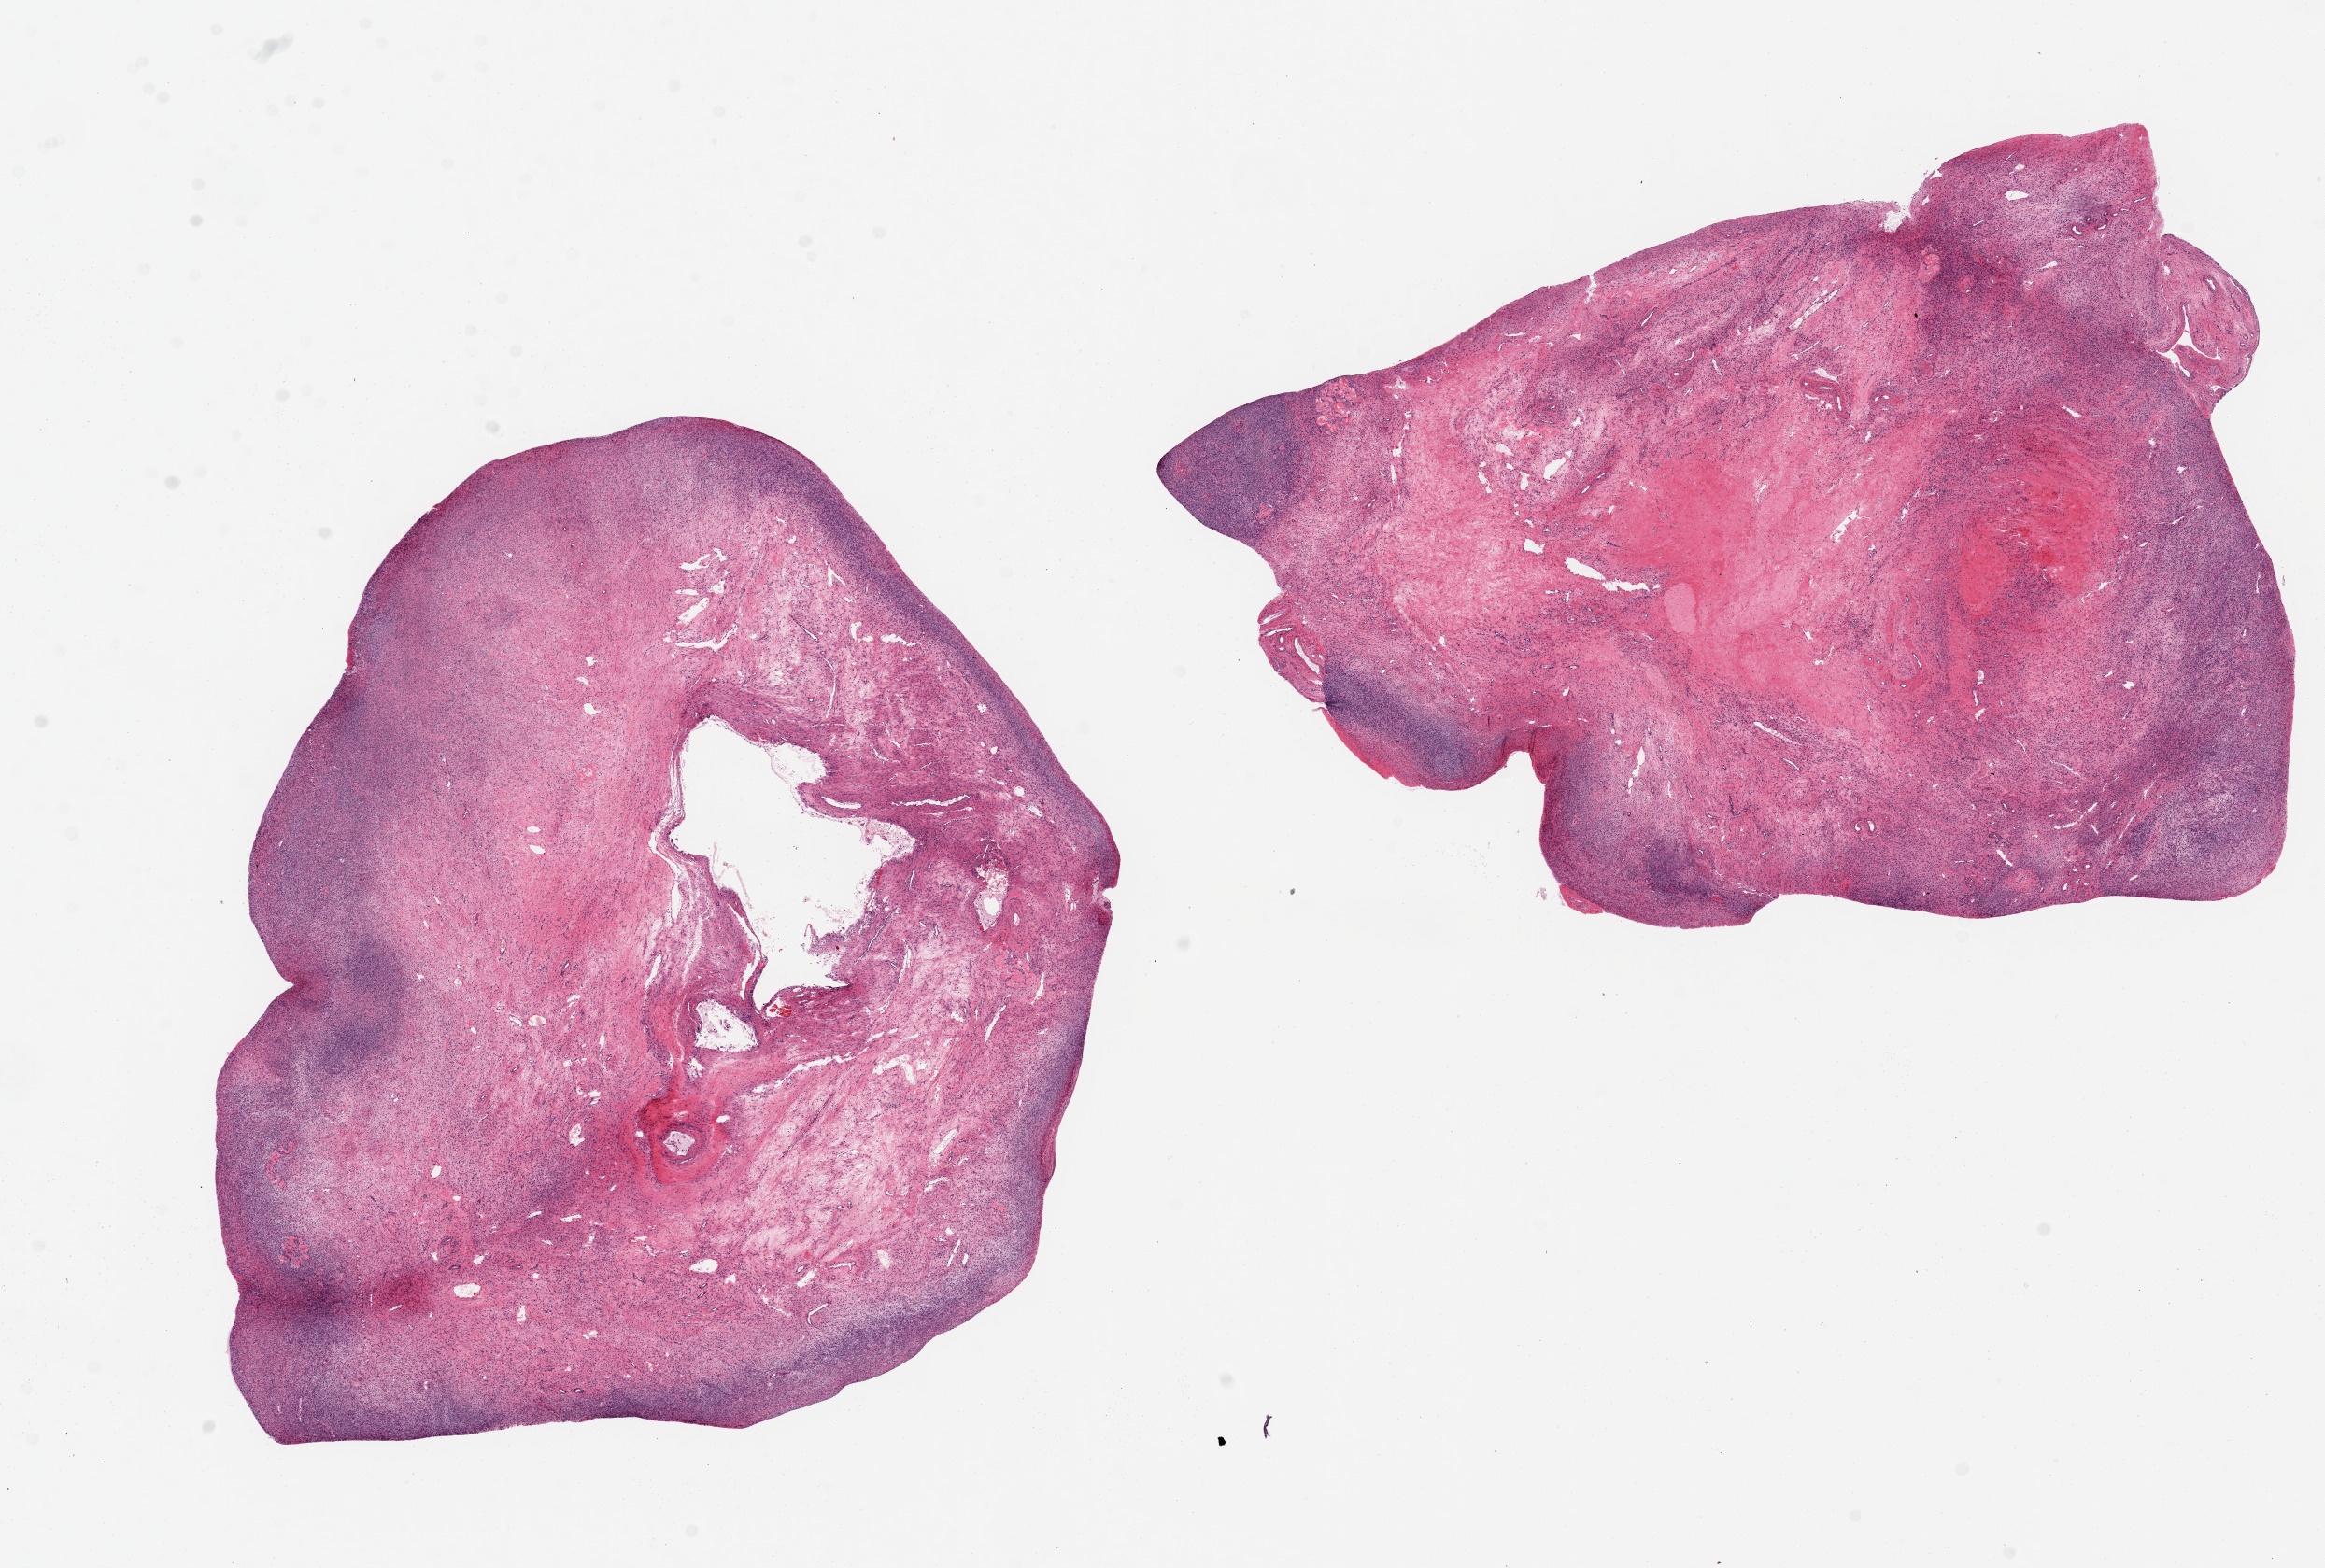
Whole-slide image, H&E stain, brightfield — low-resolution overview of the scanned area, about 19.7 x 13.3 mm (from a 20x scan), PAXgene-fixed, paraffin-embedded tissue, section of ovary (target tissue), tissue donor sample. Female donor.
Reviewer comment on this tissue sample: 2 pieces, 9x7 & 9x7mm; post menopausal atrophy.